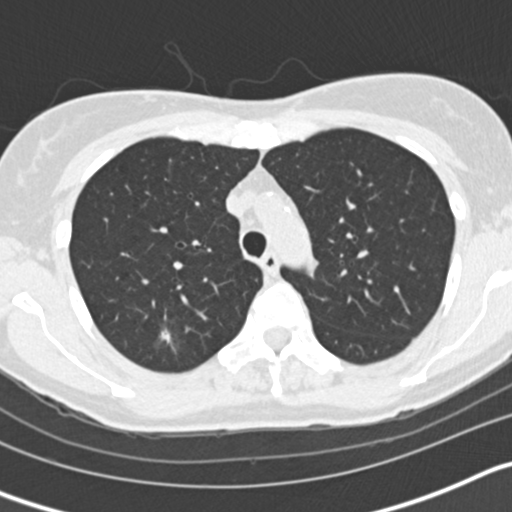
Axial slice from a low-dose chest CT screening exam. Second annual screen. Lung window (W 1500 / L -600 HU). Slice 45 of 163 in the series. 512 × 512 image matrix. Female participant, aged 58 years at enrolment. Current smoker at enrolment.
- Expert reader's lesion annotation, bounding box [x1, y1, x2, y2] px = [136, 318, 194, 366].
- The screening reader recorded 3 non-calcified nodules or masses ≥4 mm on this exam (right upper lobe, left upper lobe, left lower lobe); which of them this box marks is not recorded.
- Lung cancer was diagnosed 59 days after this screen: bronchiolo-alveolar adenocarcinoma, NOS, right upper lobe, moderately differentiated (G2), stage IA (AJCC 6th edition), 7 mm at pathology.